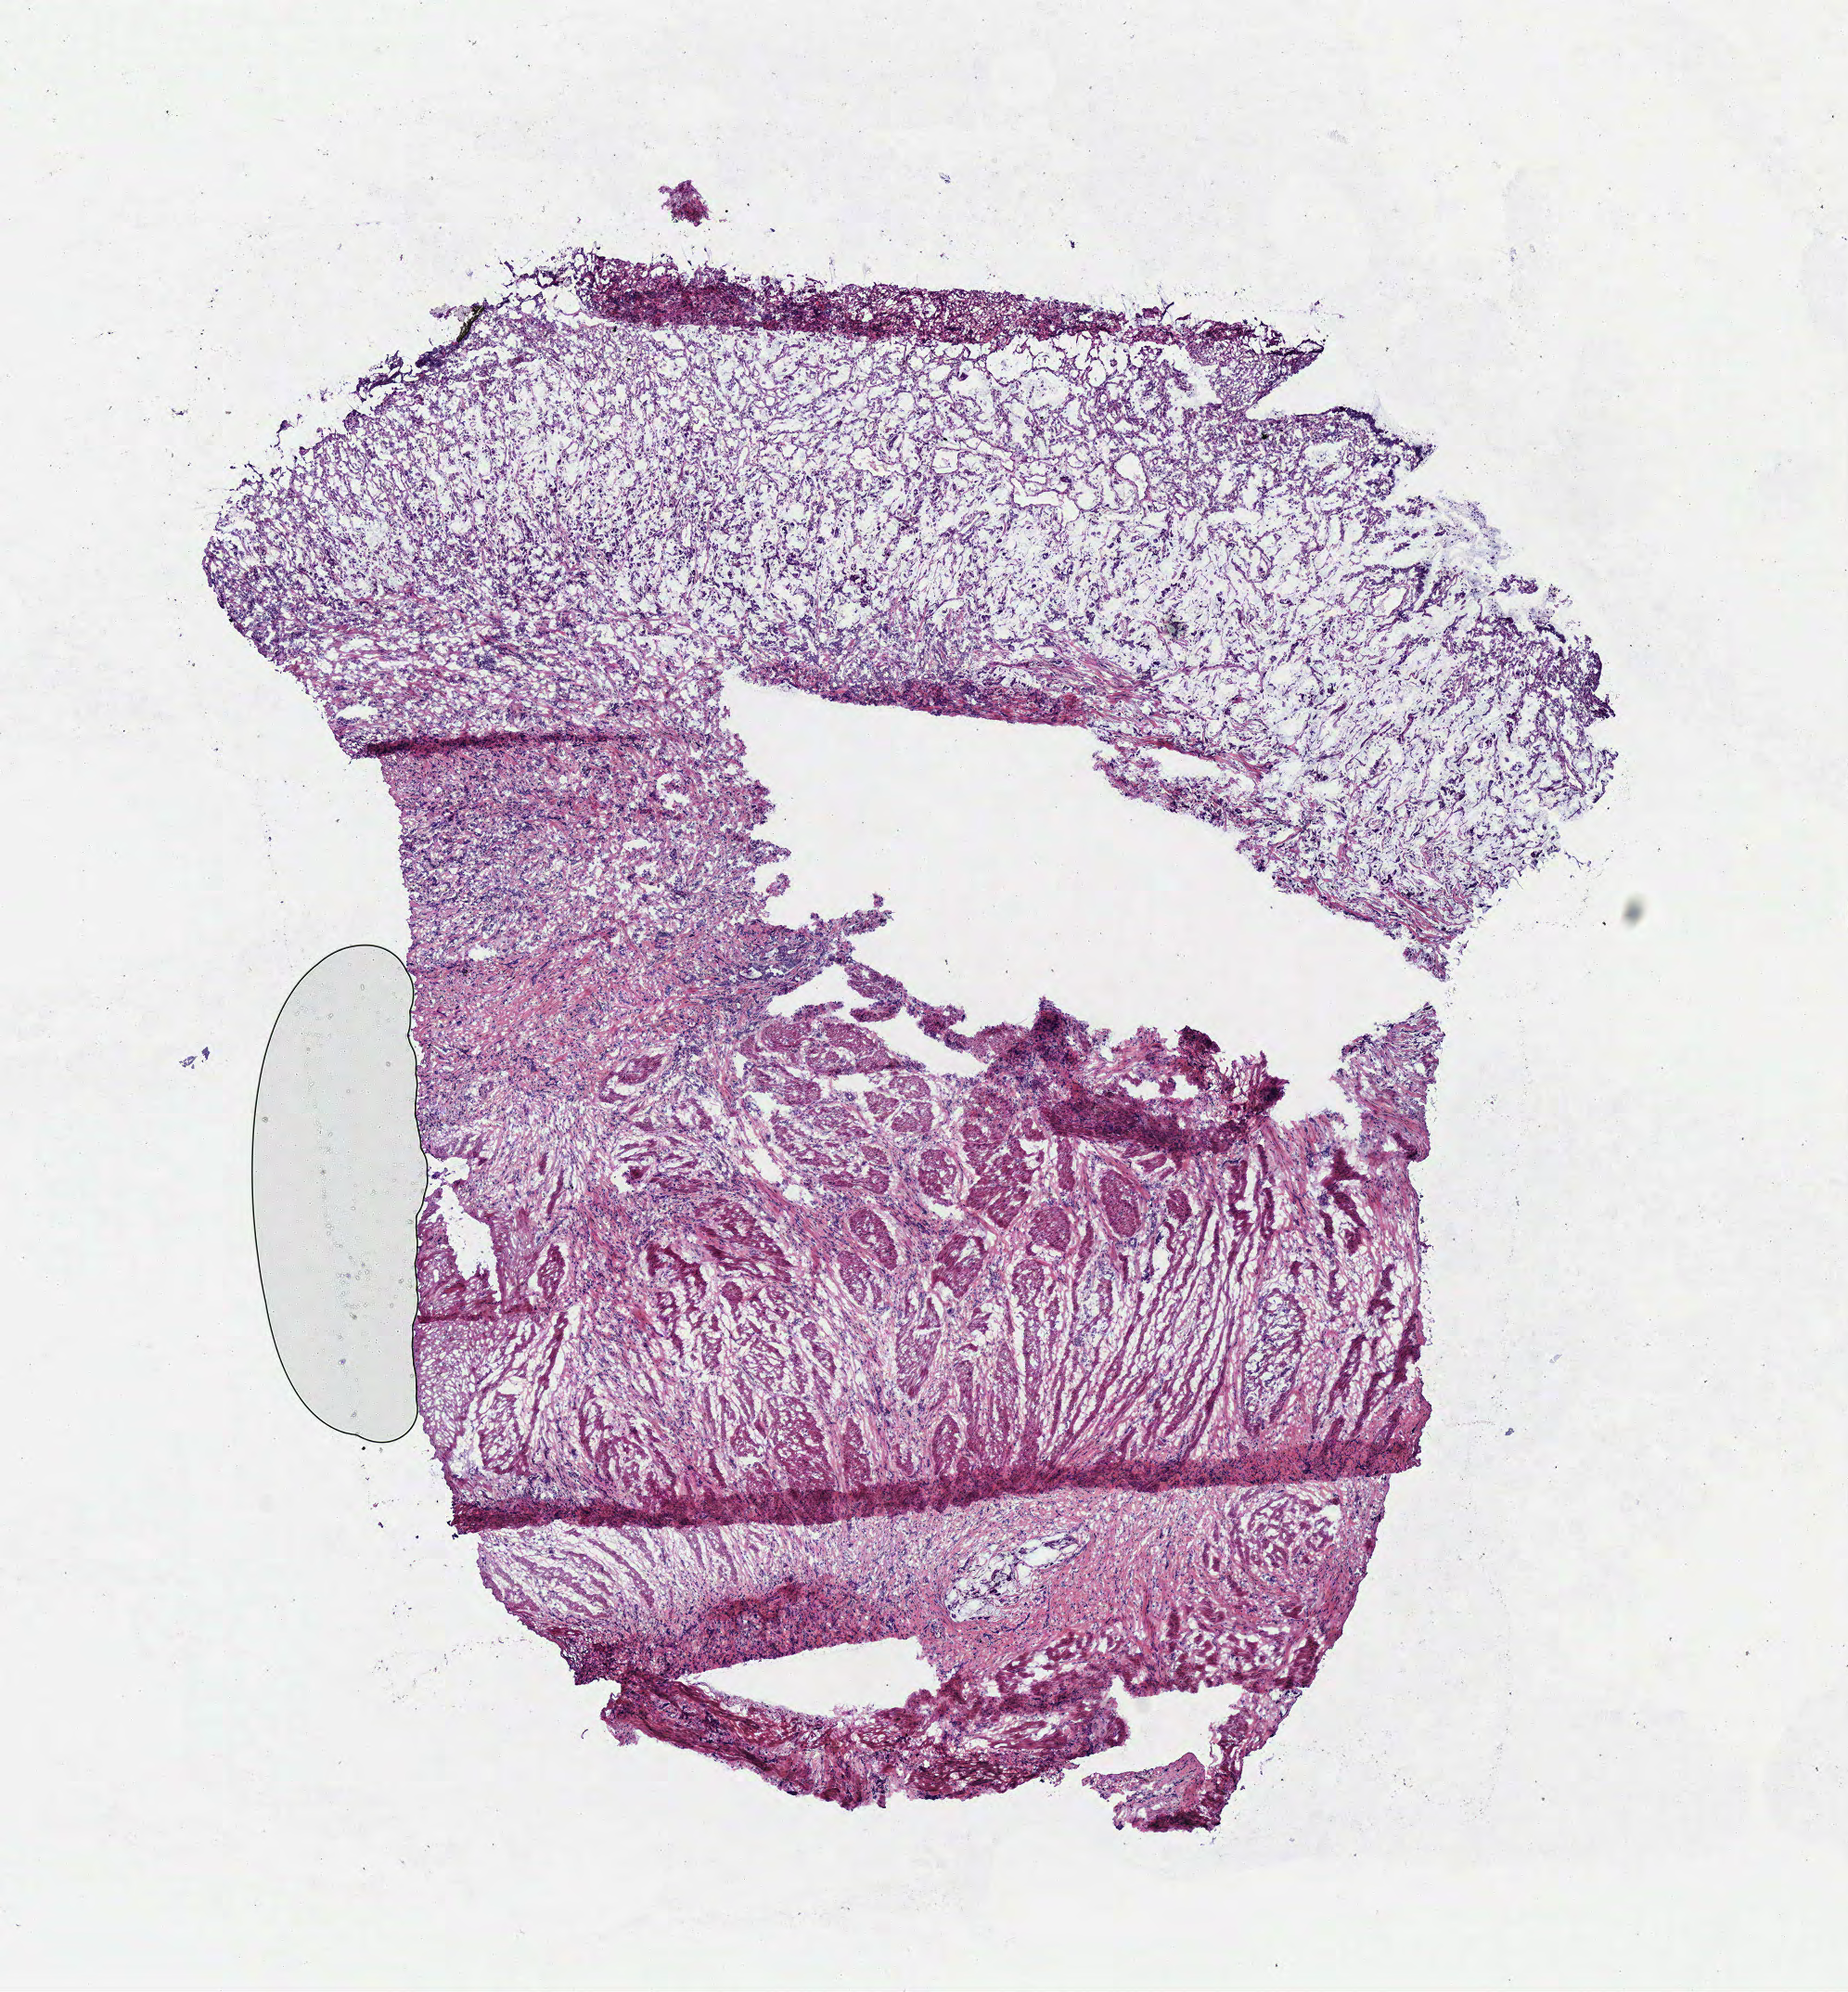
Digitized Hematoxylin and eosin (H&E) stained tissue section (whole slide), a low-resolution overview of the entire scanned area, about 7.8 x 8.4 mm (from a 40x scan), frozen section from the bottom of the tissue portion, sample: primary tumour, stomach. Patient: male, age at initial diagnosis 75 years. Histologic grade: G3 (poorly differentiated). Slide review estimates, as recorded: tumour cells 80%, tumour nuclei 80%, normal cells 0%, stromal cells 20%, necrosis 0%.
- lymph nodes positive (case pathology): 17 of 20 examined
- AJCC pathologic stage: IIIA (7th edition)
- histologic diagnosis: Carcinoma, diffuse type (cardia, NOS)